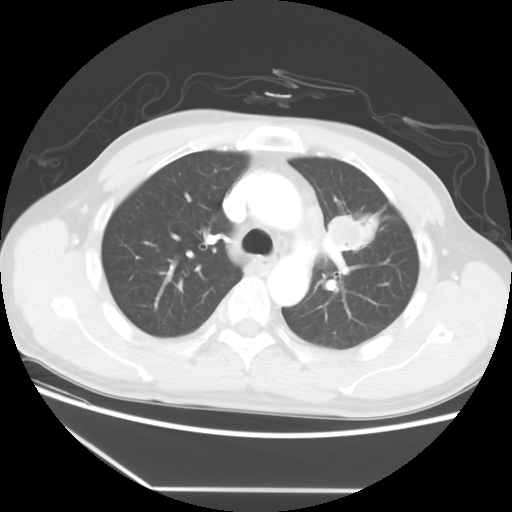
Chest CT, one axial slice. Slice 38 of 56 in the series (ordered by position). Reconstruction kernel STANDARD. Lung window (W 1500 / L -600 HU). 5 mm slice thickness. 512 × 512 image matrix, field of view 373 × 373 mm. Patient: male, 53 years. From the clinical record (not read from this slice): clinical TNM (as recorded): T2a N1 M1b.
Outlined on this slice (bounding box drawn by a radiologist):
- lung tumour (recorded histology: adenocarcinoma): bounding box <329,206,379,255> (left, top, right, bottom; pixels)